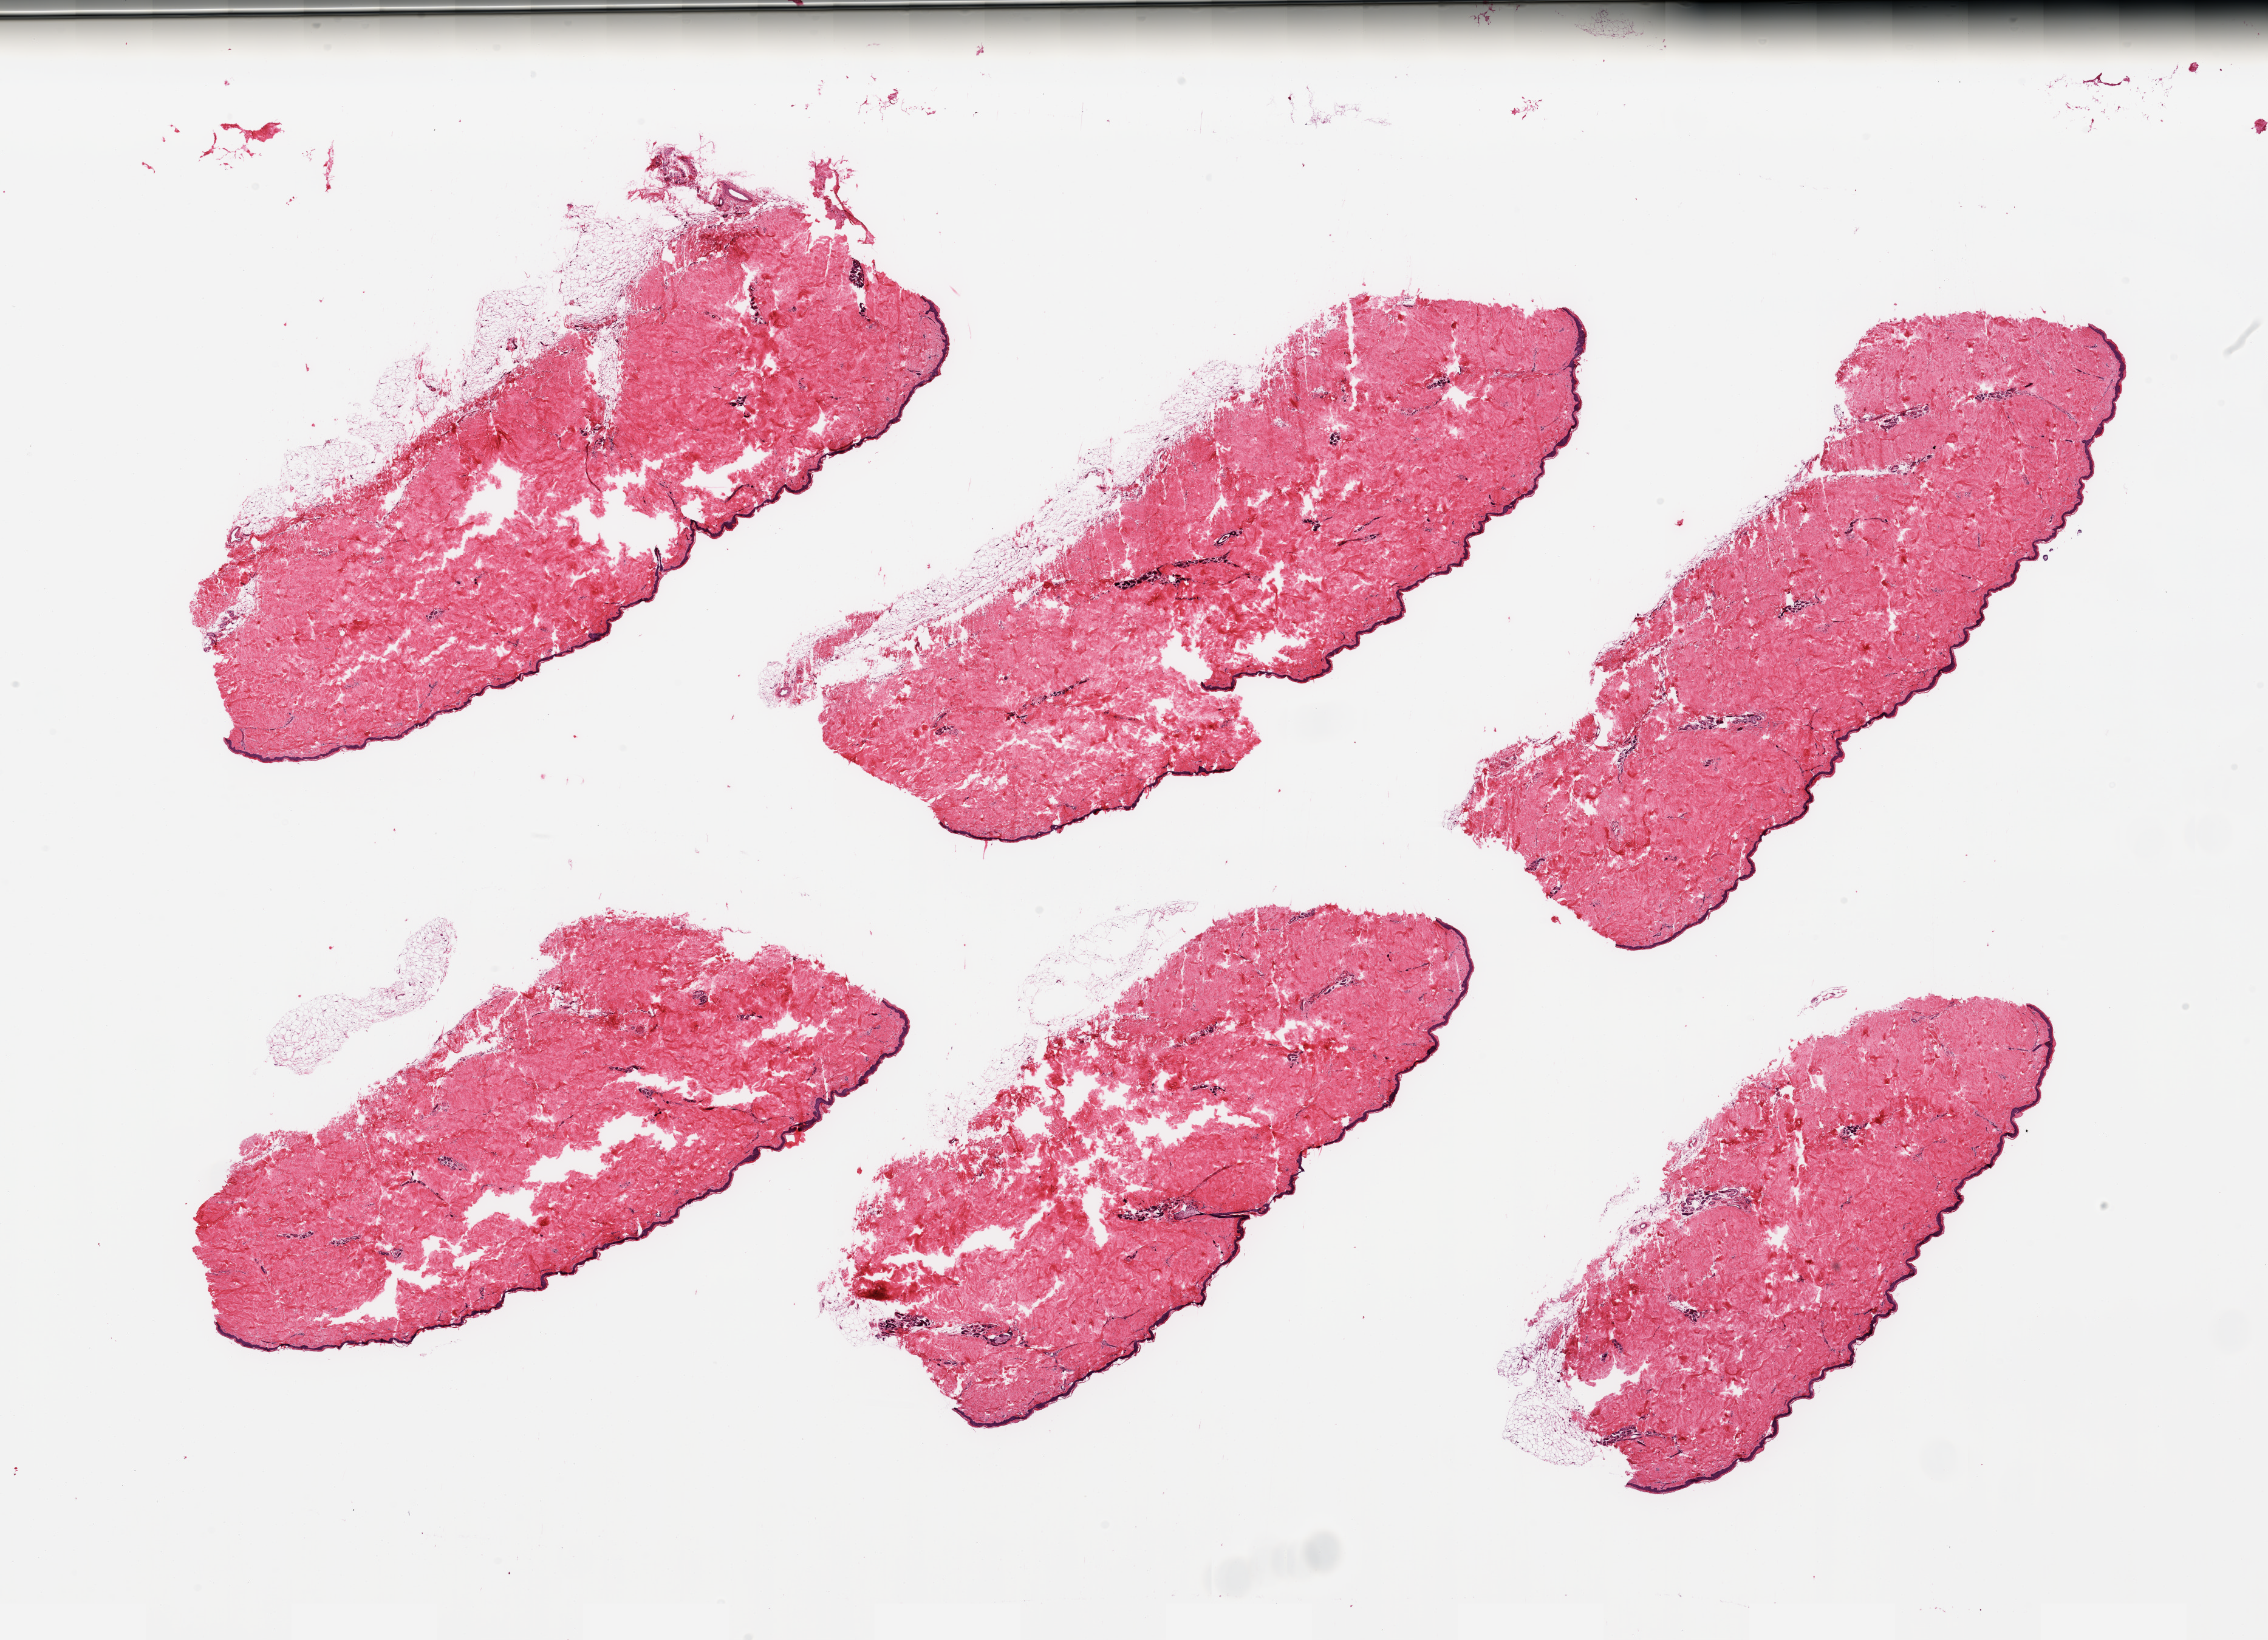
Whole-slide image, haematoxylin and eosin stain, low-resolution overview of the scanned area, about 29.5 x 21.4 mm (slide scanned at 20x). PAXgene-fixed paraffin-embedded (PFPE) section. Target tissue: skin of lower leg. Donor tissue sample. Donor: male.
Pathologist's review note for this sample: 6 pieces, adherent dermal fat up to ~1mm; squamous epithelium is ~30 microns.